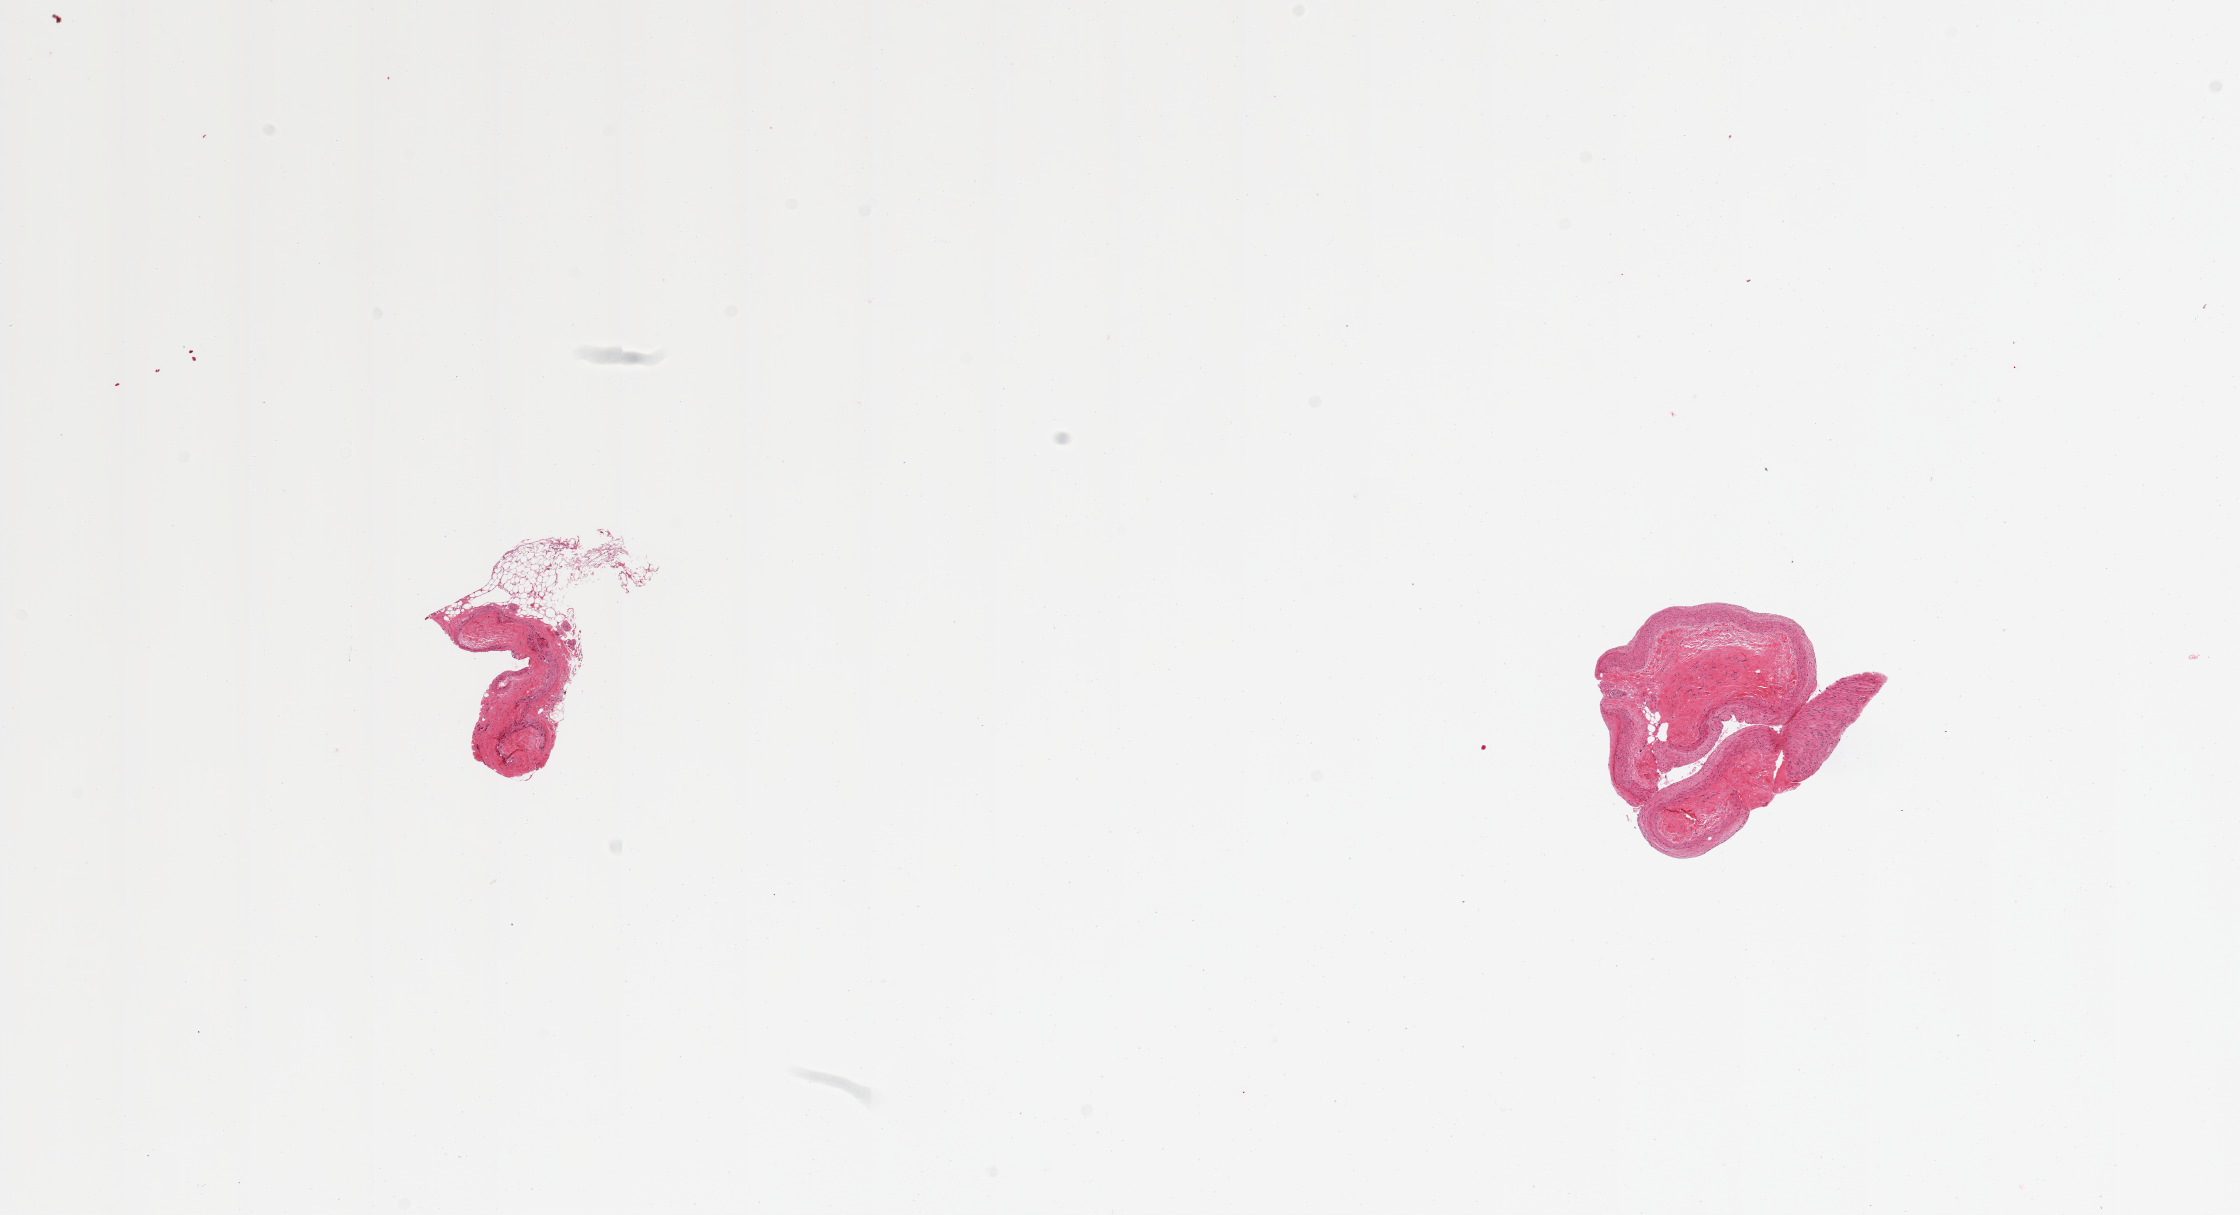
Digitized haematoxylin and eosin-stained section, whole scanned area (about 17.7 x 9.6 mm) shown as a low-resolution overview. PAXgene-fixed paraffin-embedded (PFPE) section. Section of coronary artery (target tissue). Tissue donor sample. Male donor.
Pathologist's review note for this sample: 2 pieces; 30% external fat on 1; sclerotic wall.